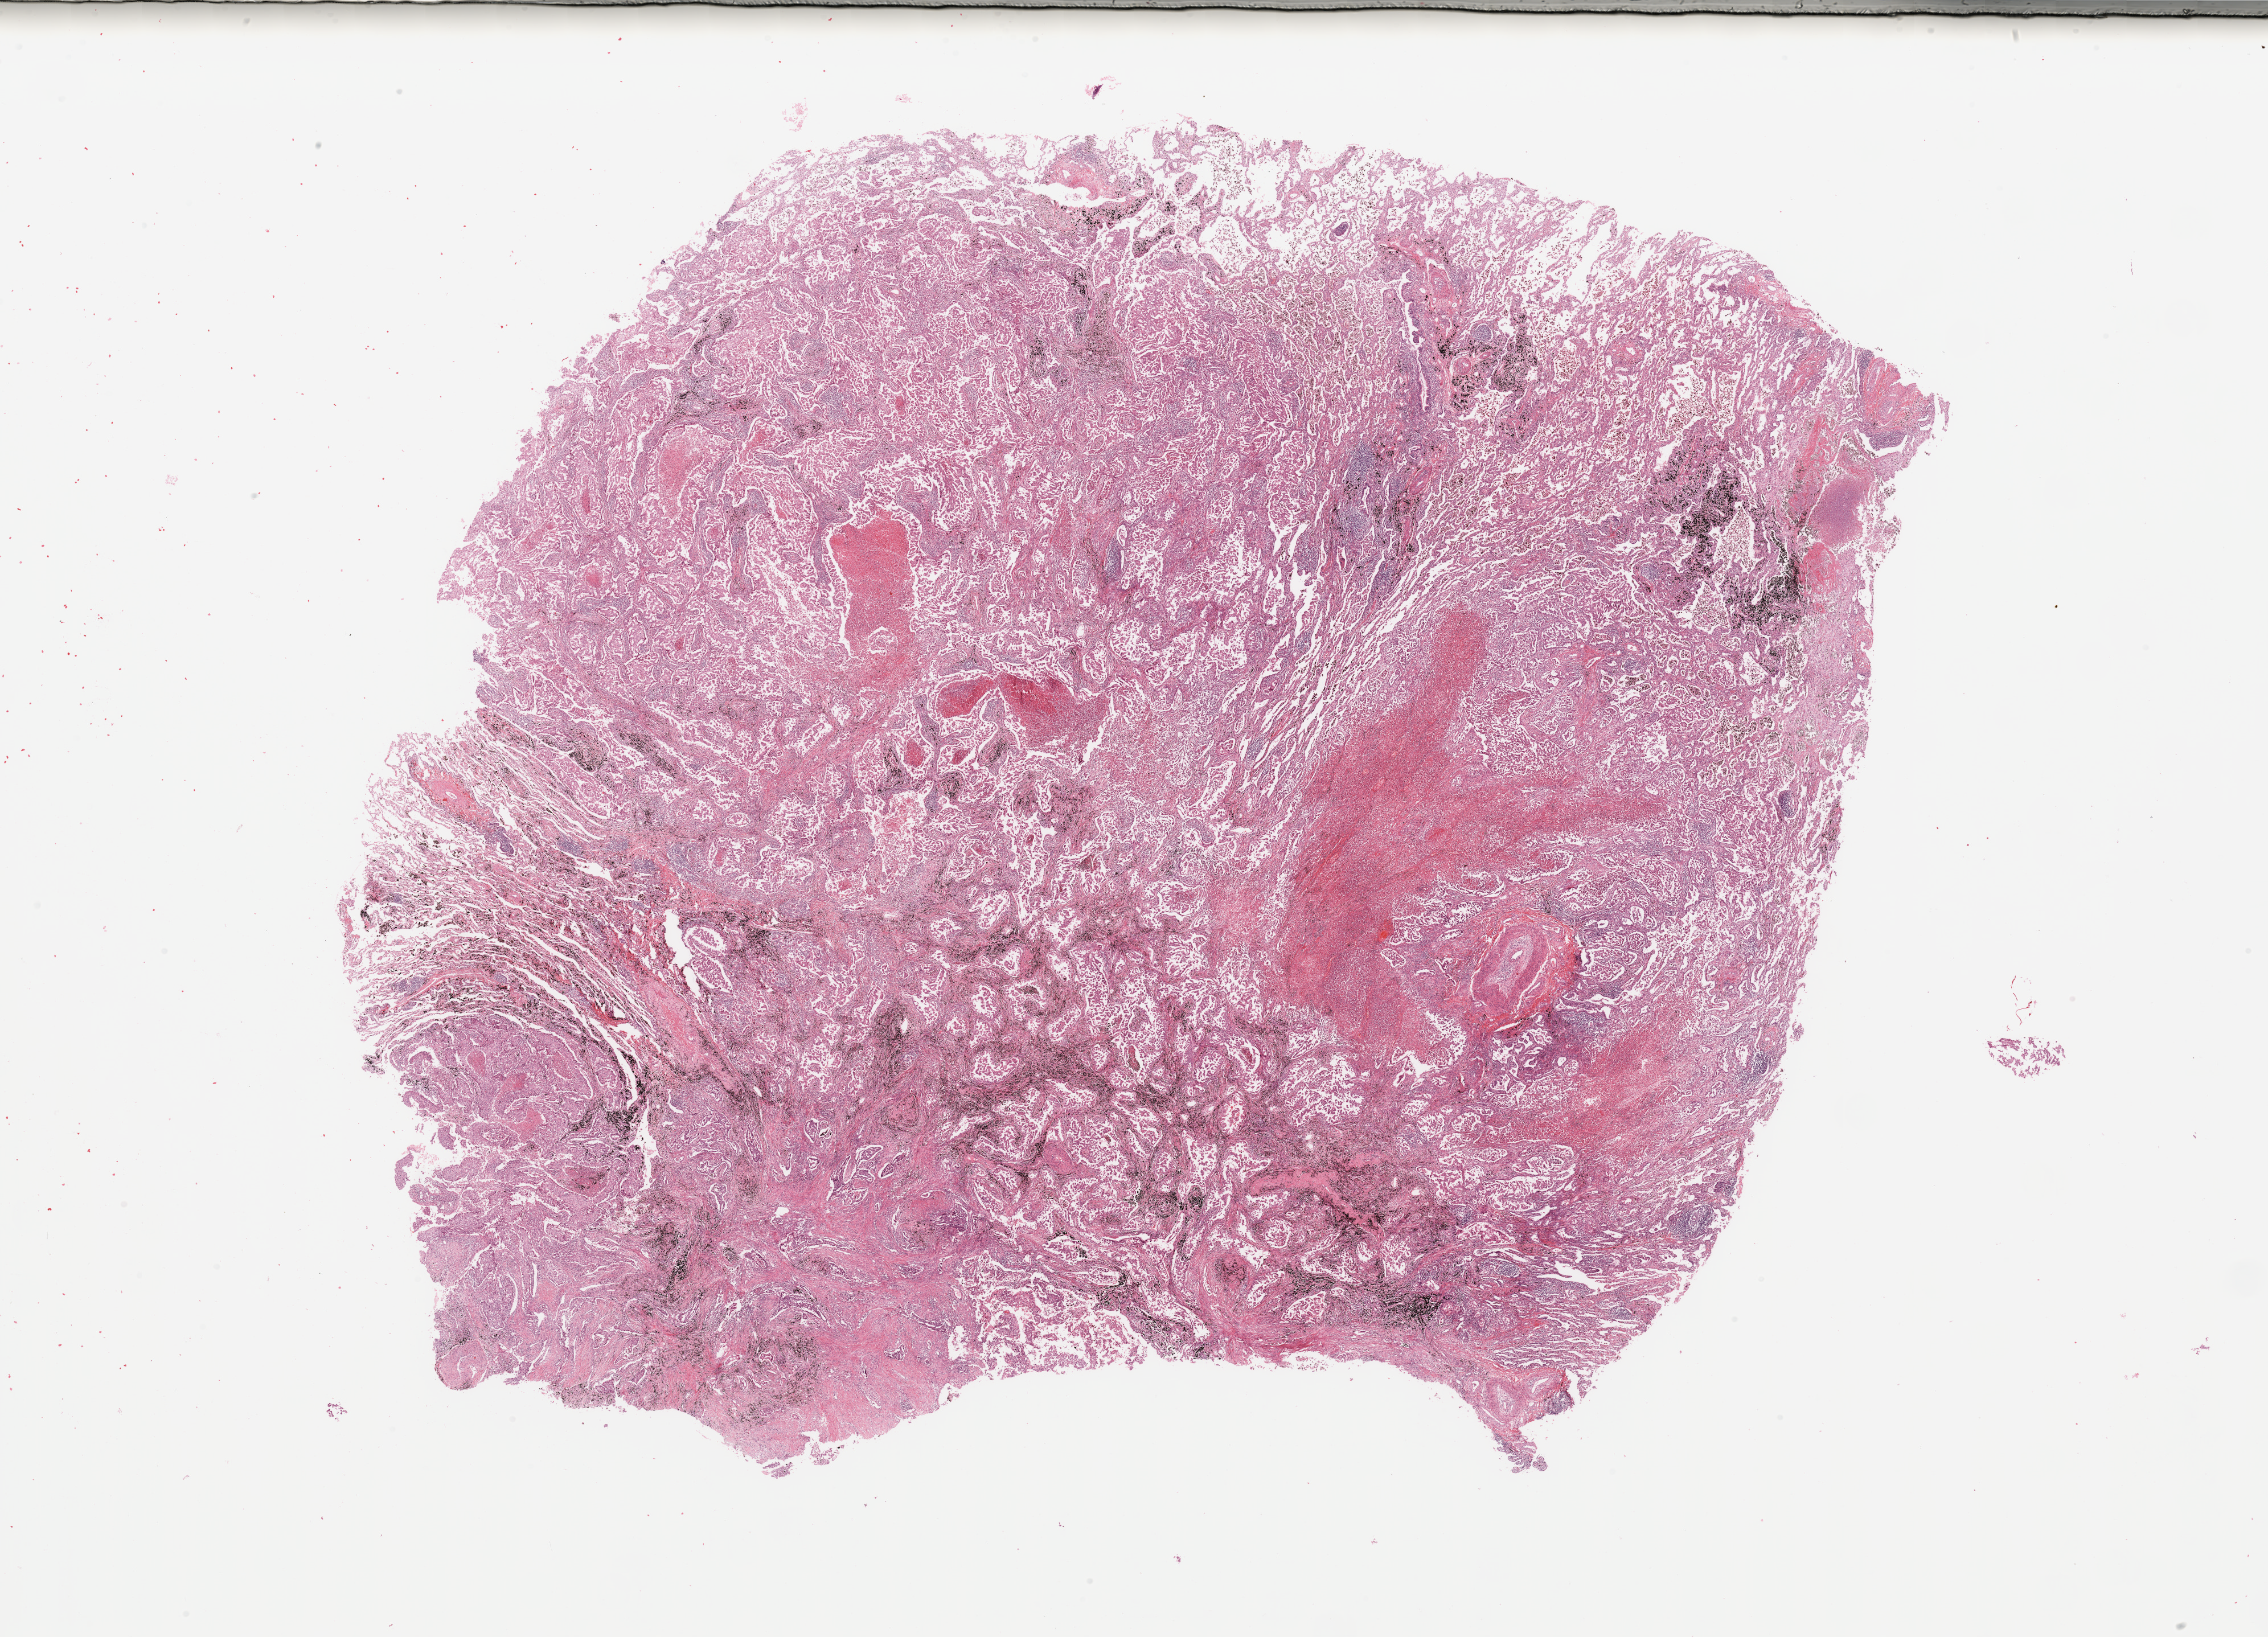
Digitized Hematoxylin and eosin (H&E) stained tissue section (whole slide) — low-resolution overview of the scanned area, about 31.5 x 22.7 mm; lung, tumour tissue. Patient: male, age 63 years. Histologic grade: G2 (moderately differentiated).
- AJCC pathologic stage: IB
- diagnosis: Adenocarcinoma, NOS